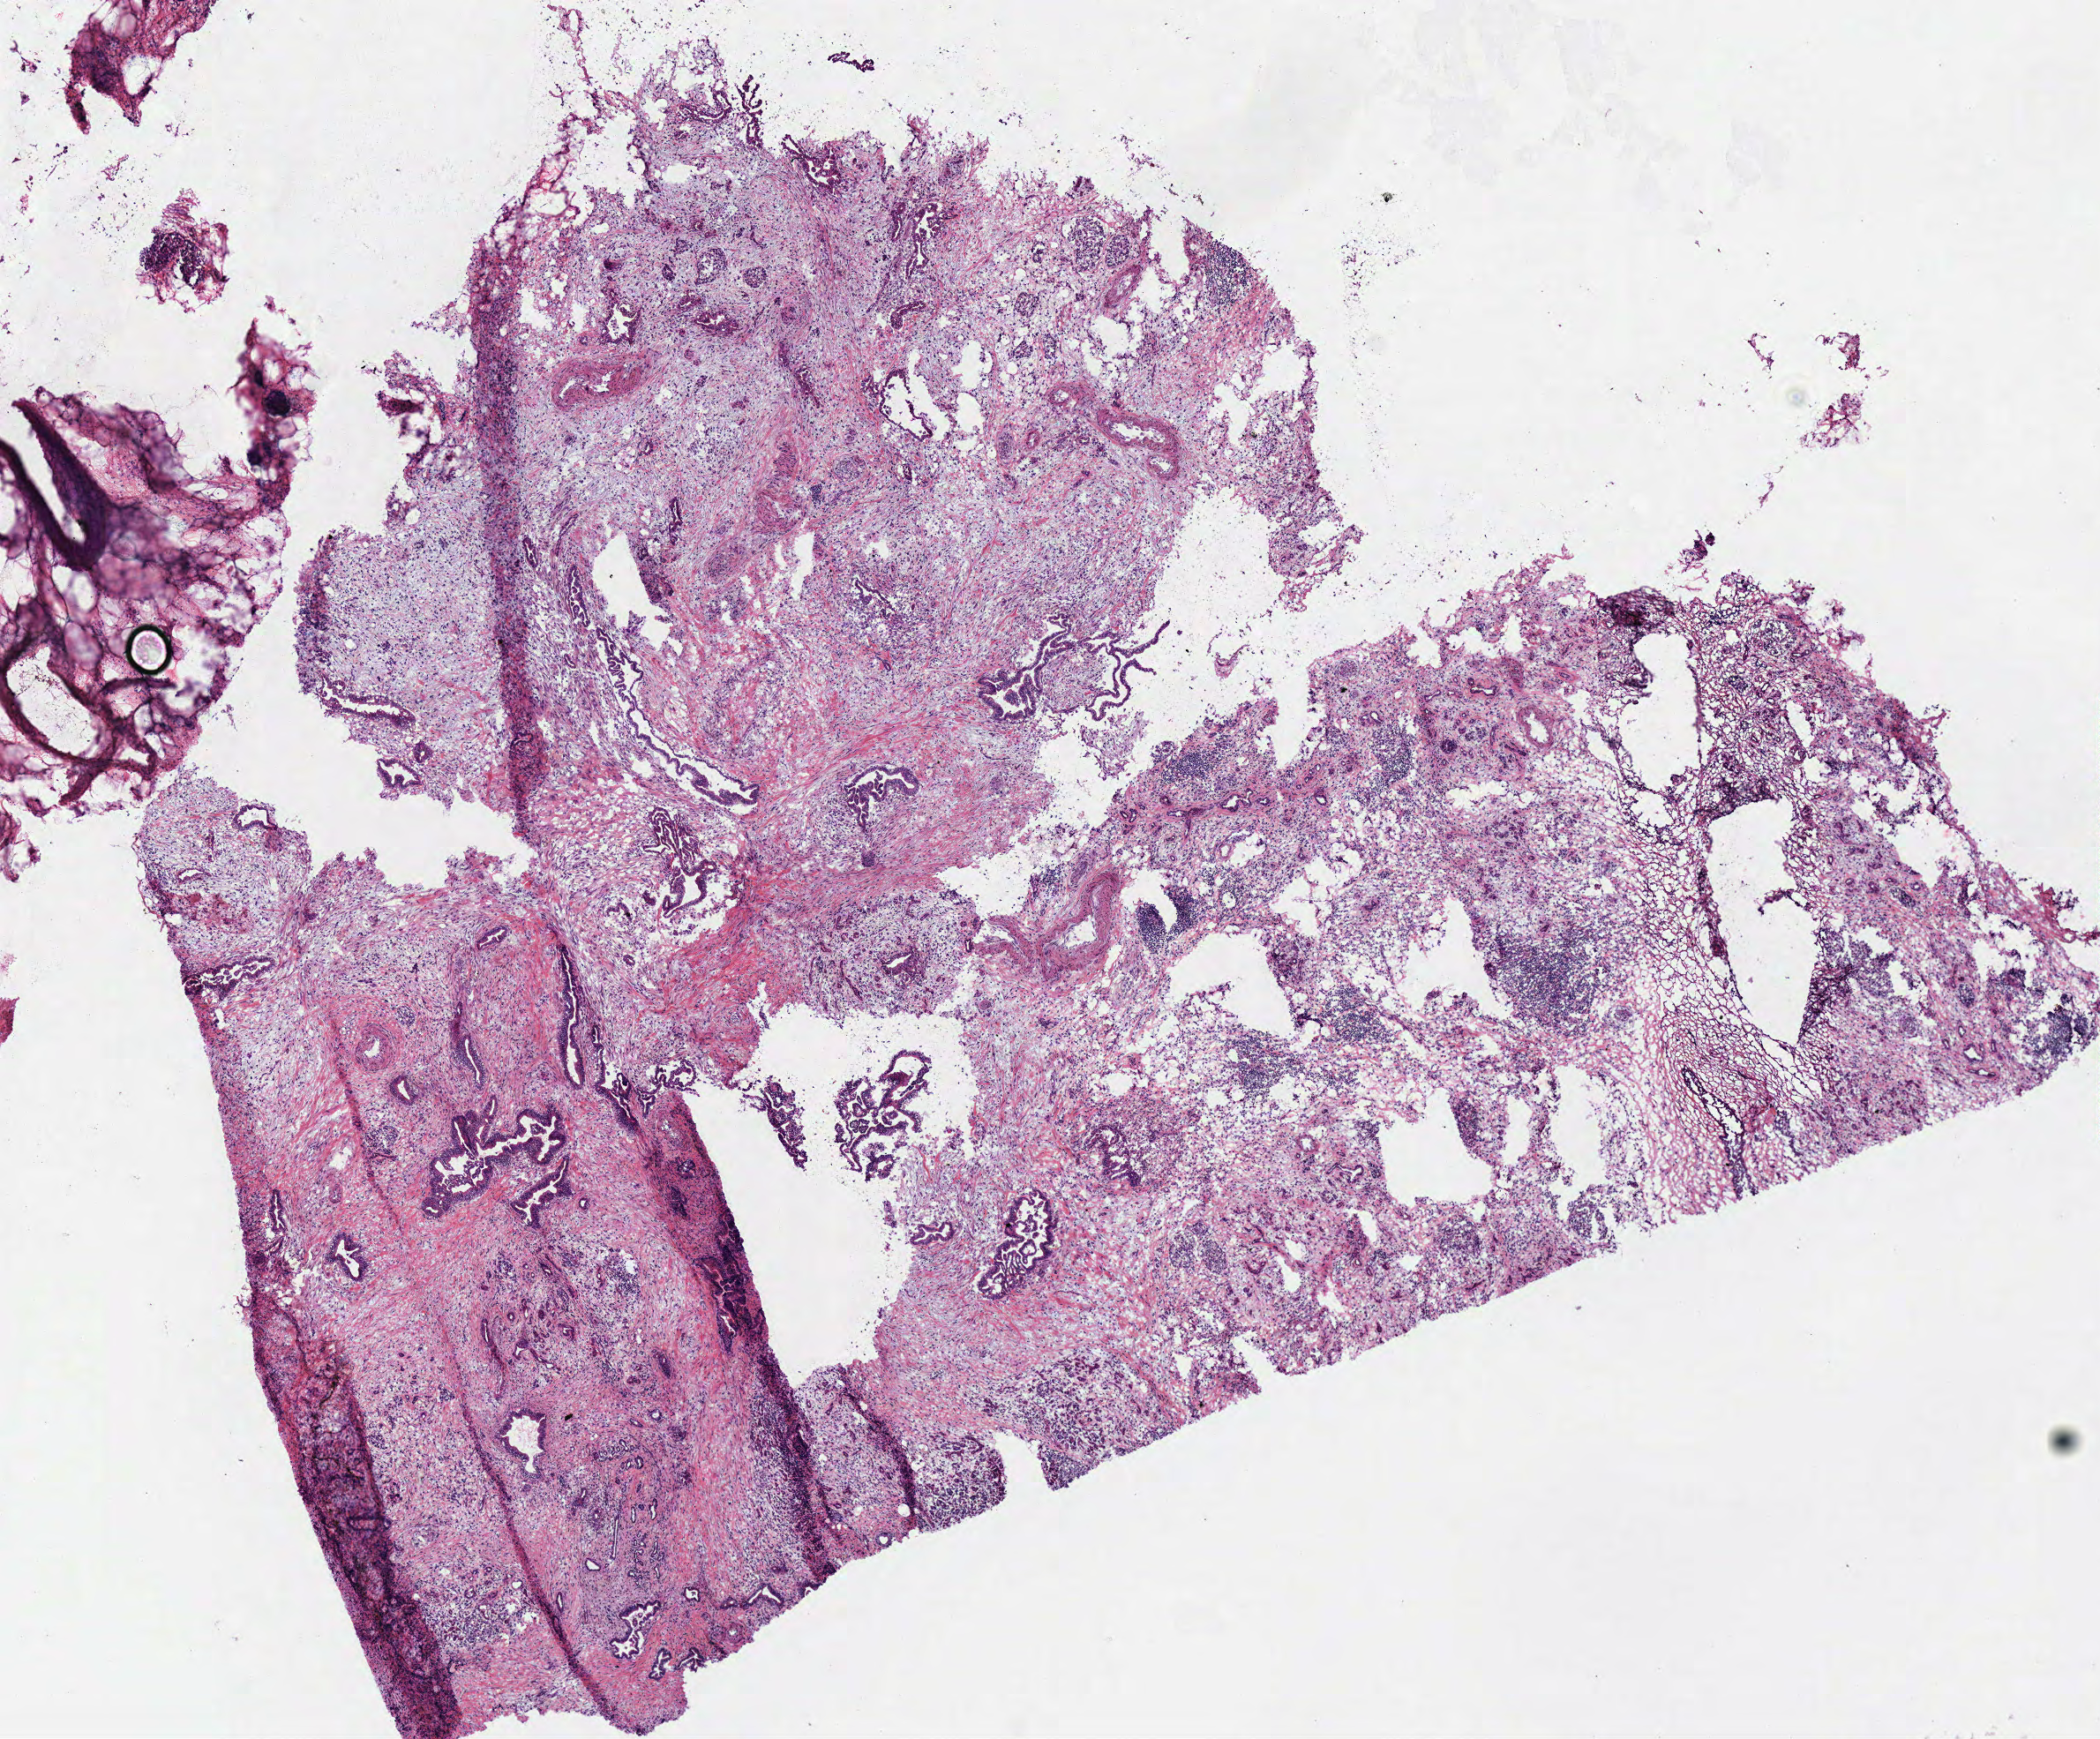
Digitized H&E tissue section (whole slide), a low-resolution overview of the entire scanned area, about 9.4 x 7.8 mm (slide scanned at 40x). Frozen section from the bottom of the tissue portion. Primary tumour sample from the pancreas. Male, age 81 years at initial diagnosis. Histologic grade: G2 (moderately differentiated). Slide review estimates, as recorded: tumour cells 50%, tumour nuclei 70%, normal cells 0%, stromal cells 50%, necrosis 0%.
* lymph nodes positive (case pathology): 0 of 5 examined
* AJCC pathologic stage: IIA
* TNM: T3 N0 M0
* histologic diagnosis: Infiltrating duct carcinoma, NOS (head of pancreas)